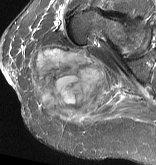
MRI of an extremity soft-tissue mass, one axial slice; position 35 of 57 along the scan axis; STIR; MR volume resampled by the dataset authors to the PET/CT grid (not the native acquisition matrix); 3.27 mm slice thickness; 156 × 165 image matrix, field of view 152 × 161 mm. Female patient. Case-level facts recorded for this patient, not image findings: histological type: epithelioid sarcoma with vascular differentiation; site of the primary tumour: right buttock.
Structures marked on this image (expert contour drawn on MRI and transferred to this co-registered scan by the dataset authors):
- gross tumour volume (mass): box from (x=29, y=46) to (x=114, y=118) px